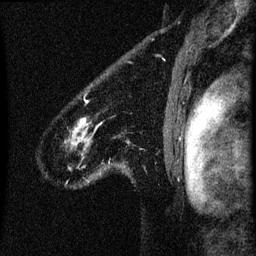
Breast MRI (dynamic contrast-enhanced), one sagittal slice. Slice 55 of 60 in the series (ordered by position). Dynamic contrast-enhanced series, image 2 of 3 at this slice position (ordered by acquisition). 1.5 T. TE 4.2 ms, TR 8 ms. 2 mm slice thickness. 256 × 256 image matrix, field of view 180 × 180 mm. Patient: female, 61 years.
Structures marked on this image (semi-automatic segmentation, software-assisted and operator-edited):
- analysis volume of interest (the breast-tissue region the enhancement analysis was run in; not a lesion): bounding box <65,86,103,183> (left, top, right, bottom; pixels)
- tumour enhancement mask (voxels above the 70 % enhancement threshold inside the analysis volume of interest): <80,100,87,123>